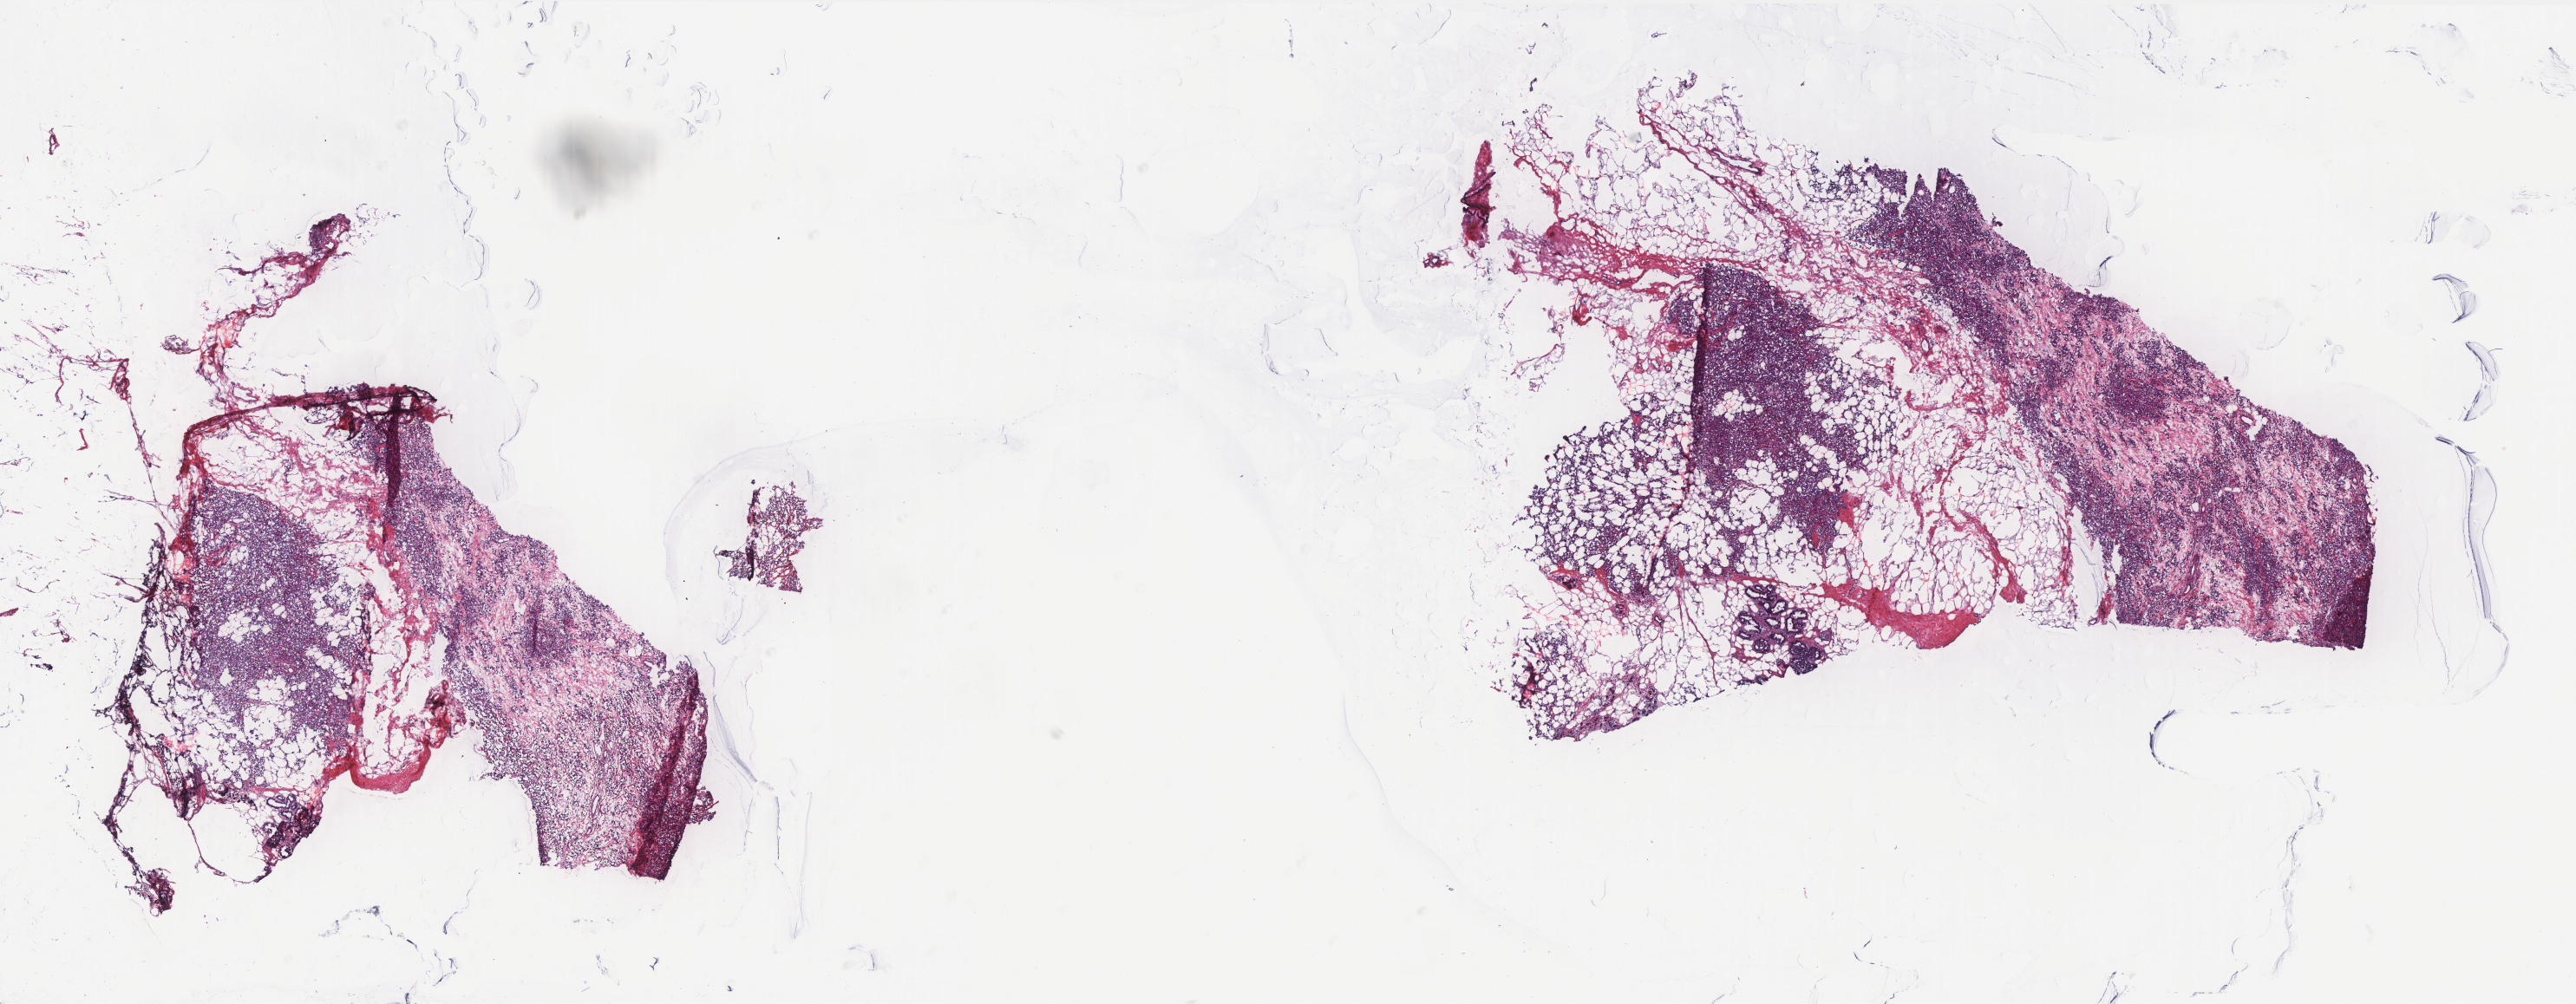
Whole-slide histology image, H&E, shown as a low-resolution overview of the whole scanned area (about 23.8 x 9.3 mm, slide scanned at 40x); frozen section from the top of the tissue portion; breast, primary tumour sample. Female, age 51 years at initial diagnosis. Pathologist review of this section (percent, as recorded): tumour cells 55%, tumour nuclei 70%, normal cells 5%, stromal cells 40%, necrosis 0%. Infiltration values recorded for this section: lymphocyte infiltration 0%, monocyte infiltration 0%, neutrophil infiltration 0%.
• laterality: right
• AJCC pathologic stage: IIB (6th edition)
• pathologic diagnosis: Lobular carcinoma, NOS
• lymph nodes positive (case pathology): 0 of 13 examined